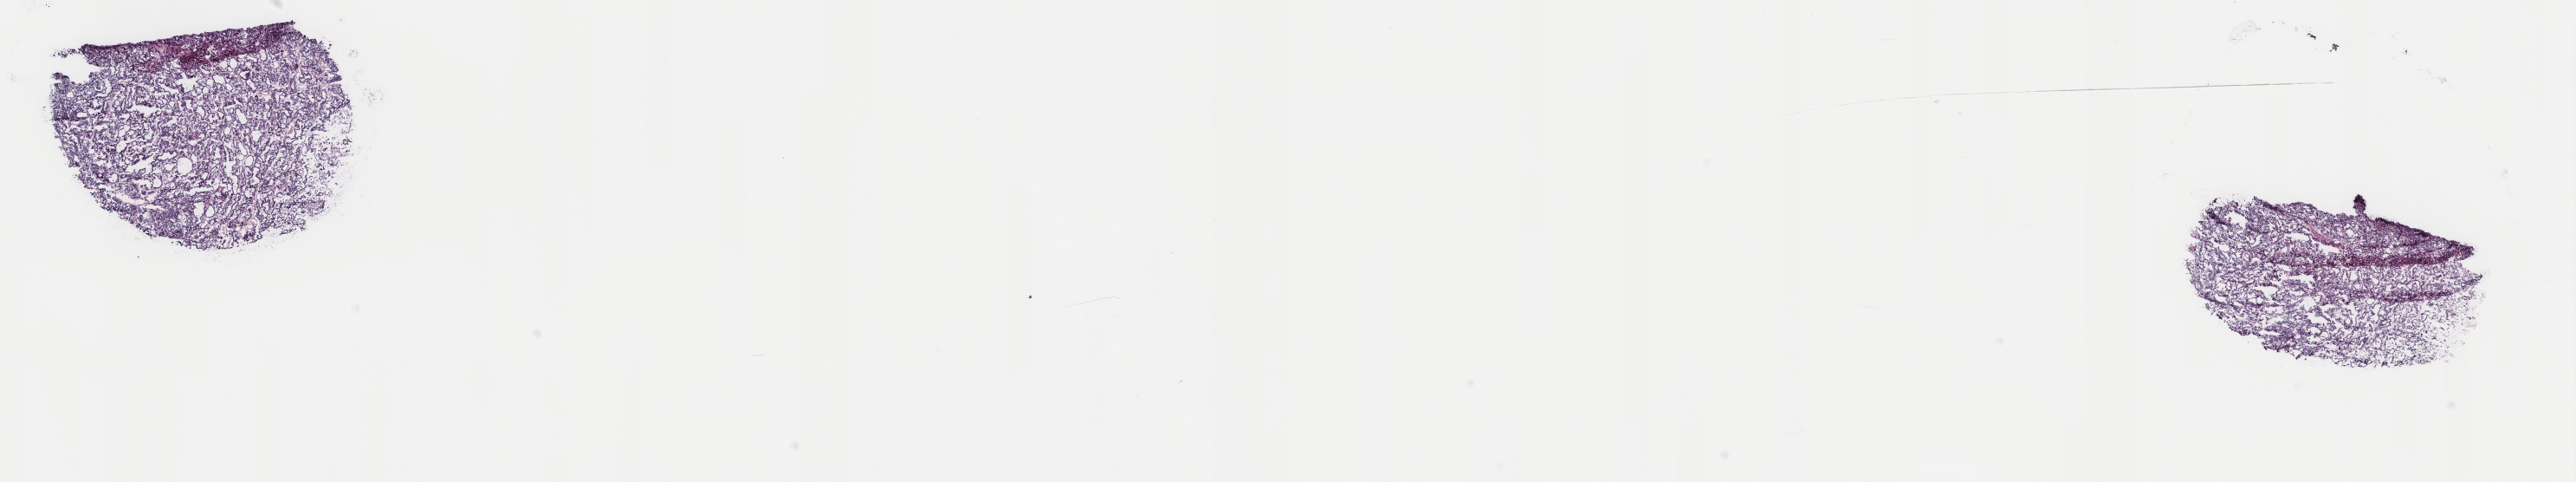
Whole-slide histology image, H&E-stained, shown as a low-resolution overview of the whole scanned area (about 23.6 x 4.4 mm). Frozen section. Metastatic tumour sample. Female, age 19 years at initial diagnosis. Composition of this section per pathologist review: tumour cells 90%, tumour nuclei 90%, normal cells 0%, stromal cells 10%, necrosis 0%. Infiltration values recorded for this section: lymphocyte infiltration 1%, monocyte infiltration 0%, neutrophil infiltration 0%.
This section: metastatic tumour tissue. Patient diagnosis: Papillary adenocarcinoma, NOS (primary site: thyroid gland).